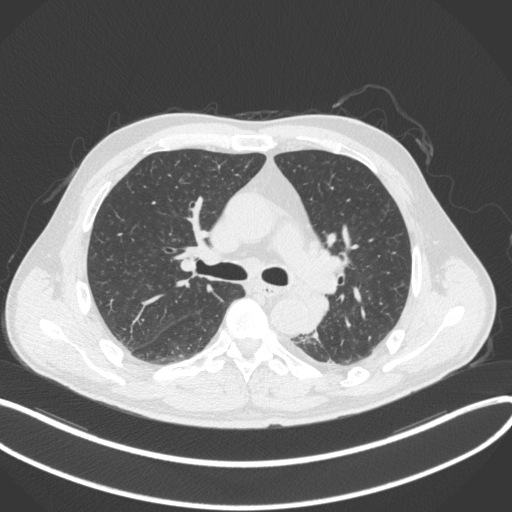
Chest CT, one axial slice. Slice 217 of 328 in the series (ordered by position). Reconstruction kernel B31f. 120 kVp. Lung window (W 1500 / L -600 HU). 1 mm slice thickness. 512 × 512 image matrix, field of view 400 × 400 mm. Male patient, age 59 years. From the clinical record (not read from this slice): clinical TNM (as recorded): T2a N2 M0.
Outlined on this slice (bounding box drawn by a radiologist):
- lung tumour (recorded histology: squamous cell carcinoma): bounding box (x1, y1, x2, y2) in pixels: (306, 289, 331, 325)